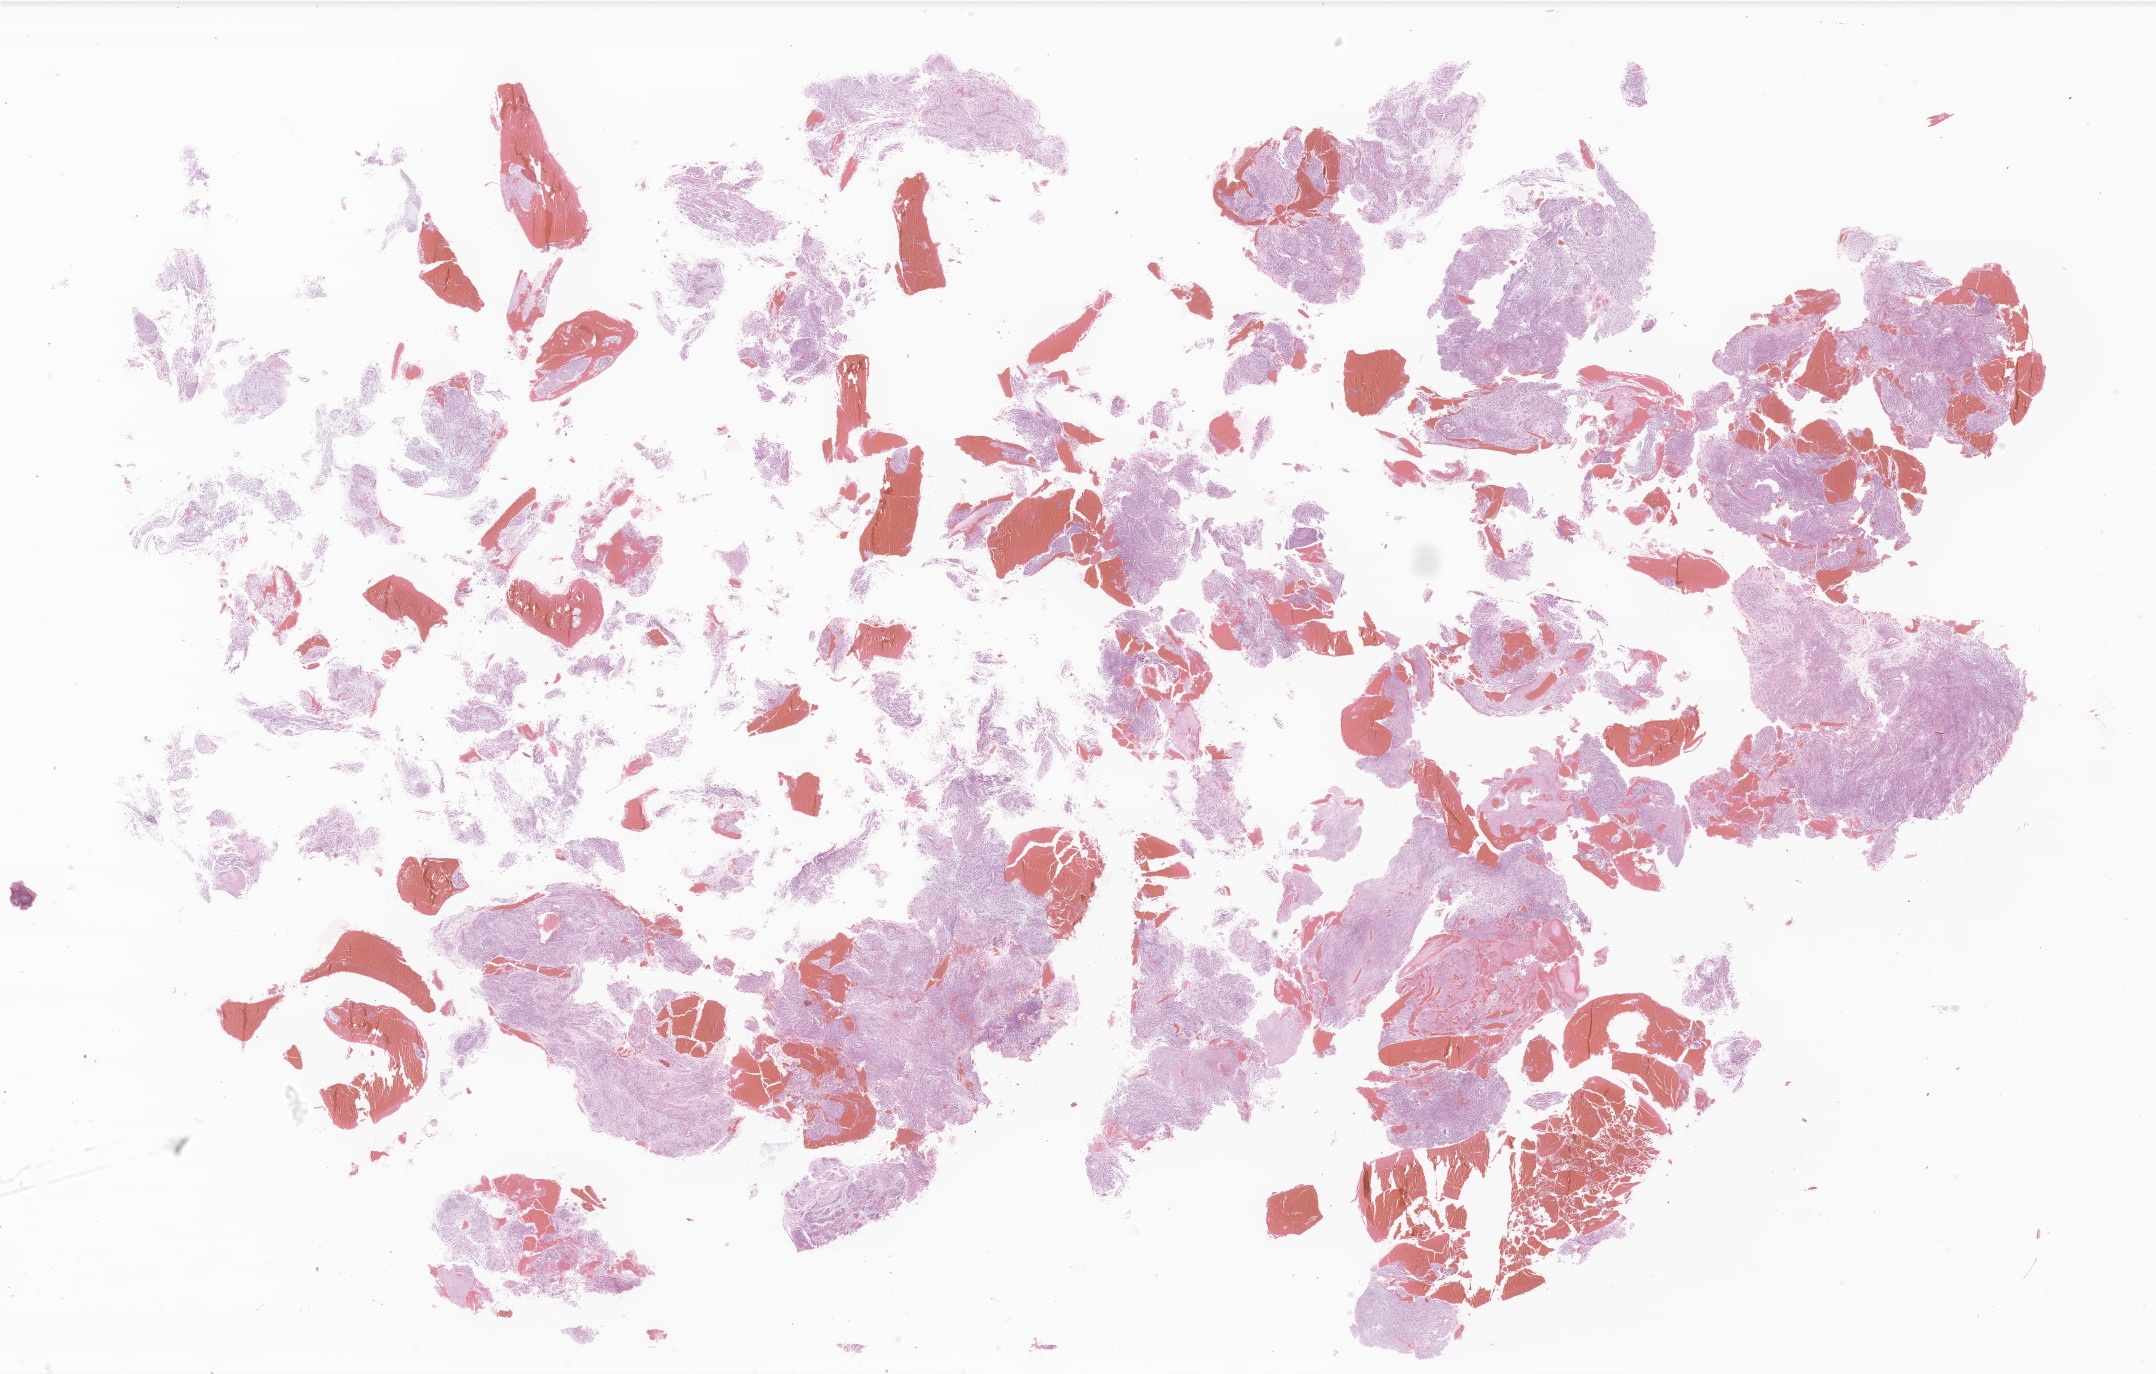
Digitized haematoxylin and eosin-stained section of tumor tissue from the brain — whole scanned area (about 36.4 x 23.2 mm) shown as a low-resolution overview, formalin-fixed paraffin-embedded section. Male patient, age 49 months (4 years 1 month).
Recorded diagnosis: Pilocytic astrocytoma.